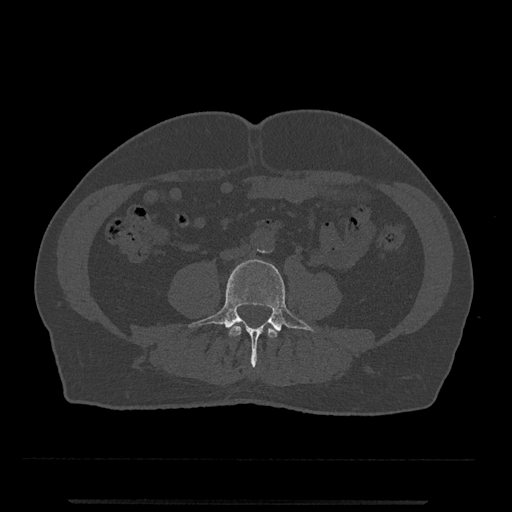
CT including the spine, one axial slice. Position 147 of 797 along the scan axis. 120 kVp. Bone window (W 1800 / L 400 HU). 0.5 mm slice thickness. 512 × 512 image matrix, field of view 419 × 419 mm. Male patient, age 63 years. From the clinical record (not read from this slice): primary cancer: prostate.
Annotated regions visible in this slice (semi-automatic segmentation, software-assisted and operator-edited):
- L3 vertebra: bounding box <228,325,278,338> (left, top, right, bottom; pixels)
- L4 vertebra: <189,259,314,367>